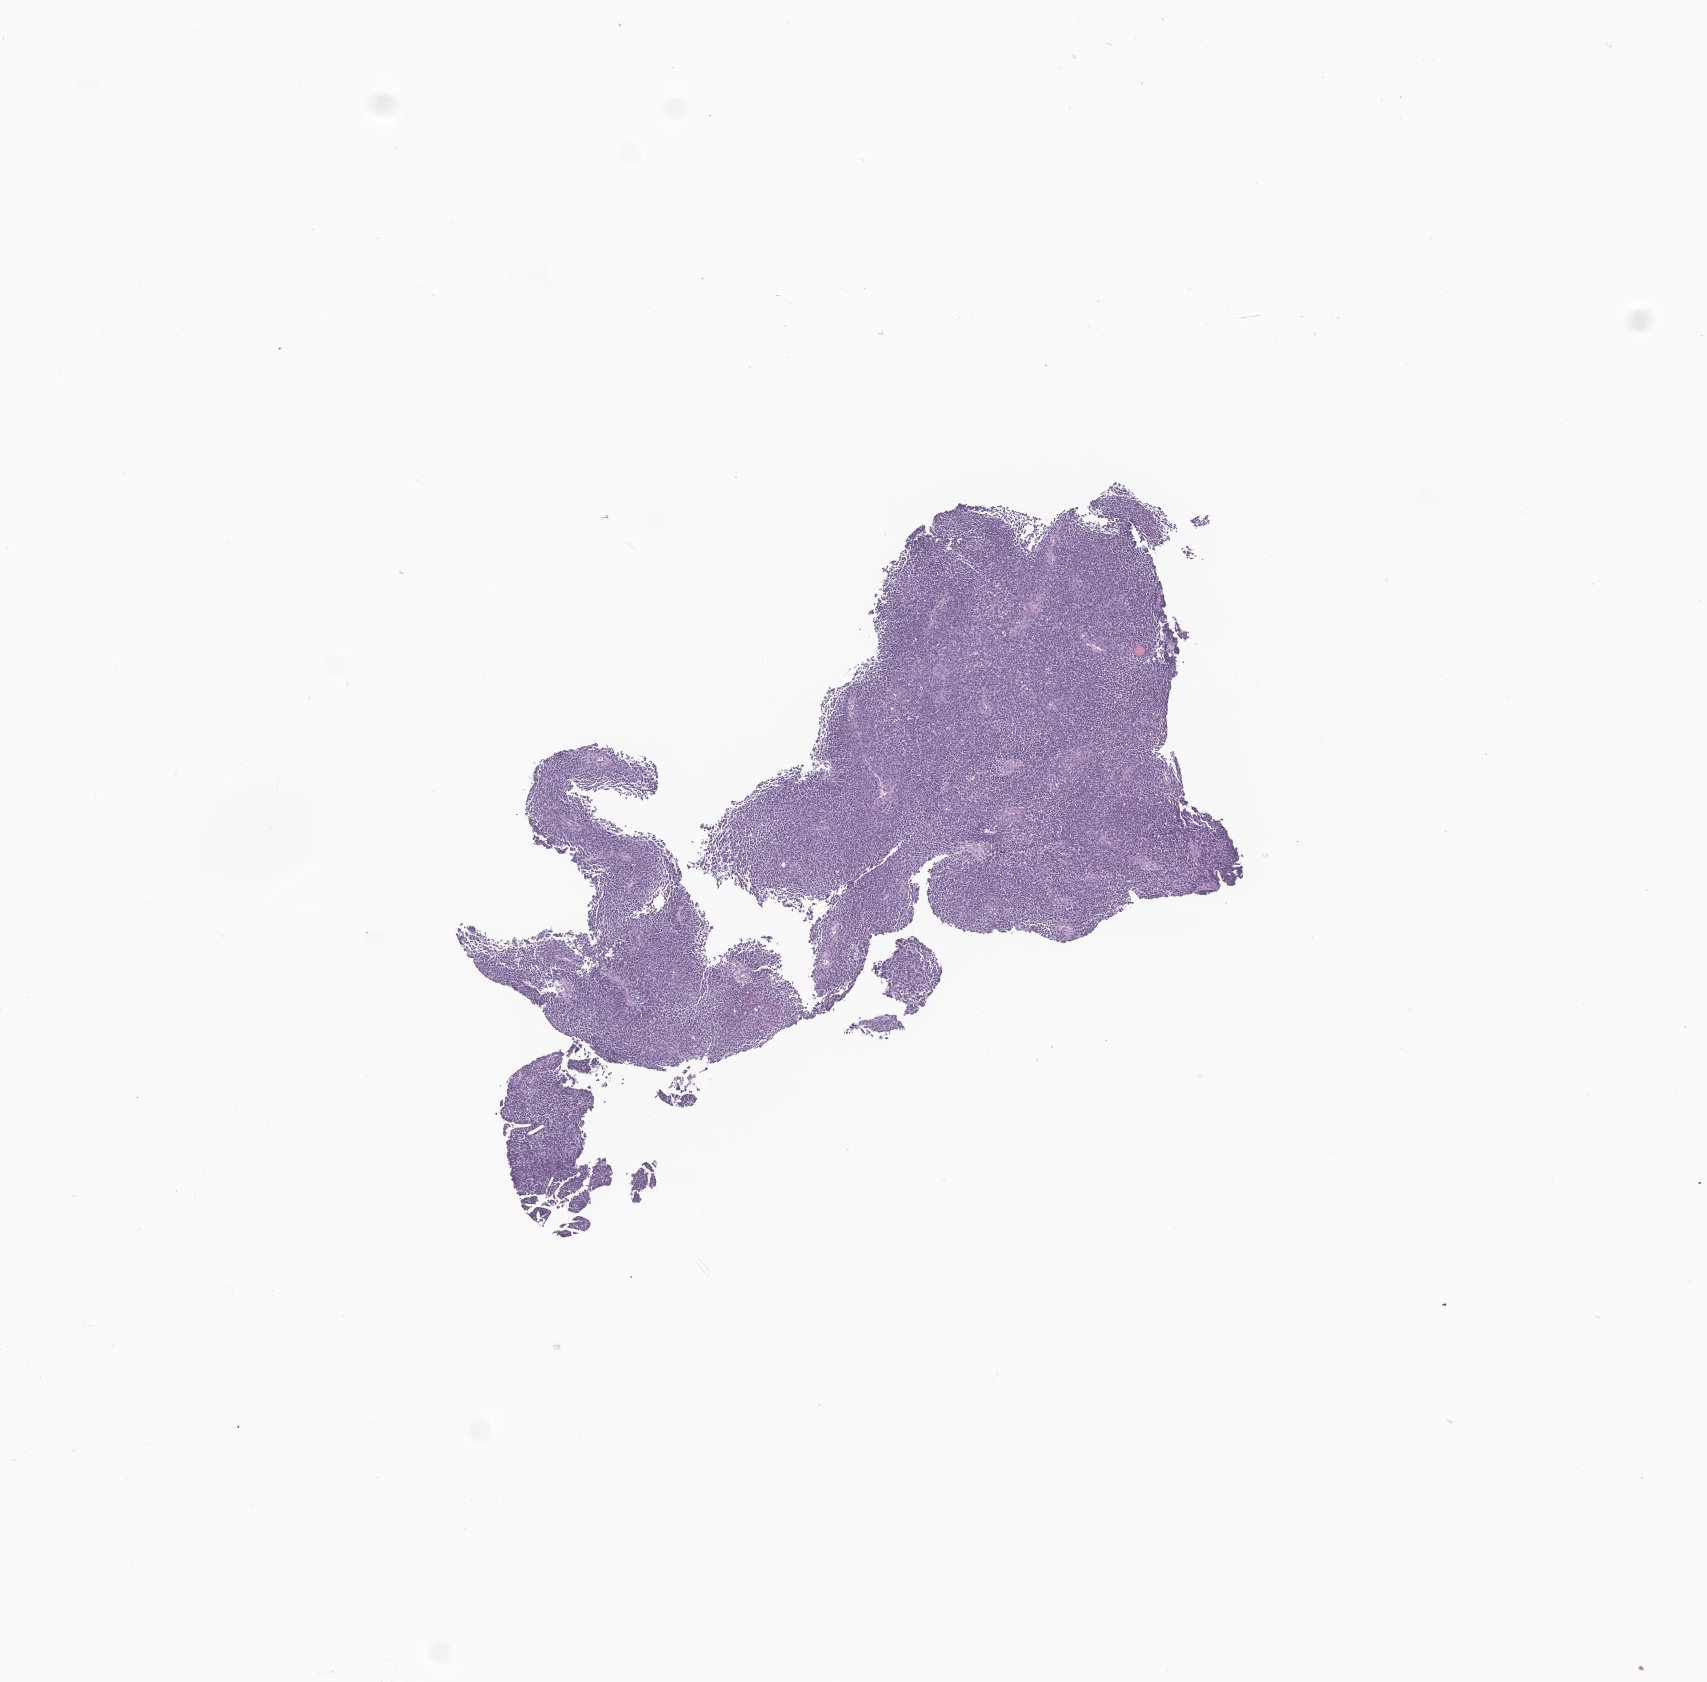
Whole-slide image, hematoxylin and eosin (H&E) stain of tumor tissue from the orbit — whole scanned area (about 7.2 x 7.1 mm) shown as a low-resolution overview. Formalin-fixed paraffin-embedded section. Male patient, age 79 months.
Diagnosis (ICD-O-3 morphology term): Embryonal rhabdomyosarcoma, NOS.